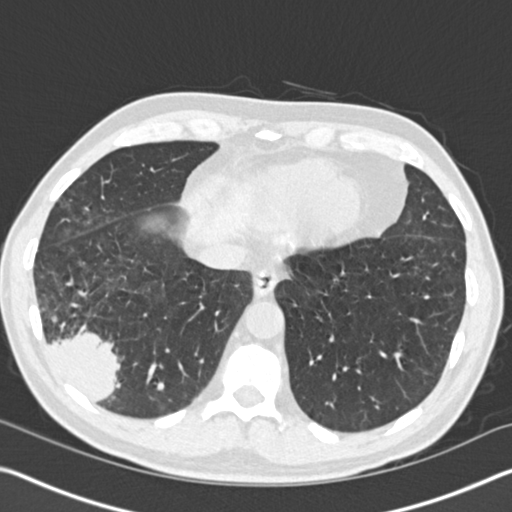
Axial slice from a low-dose chest CT screening exam. Baseline screening round. Lung window (W 1500 / L -600 HU). 2 mm slice thickness. Slice 117 of 161 in the series. 512 × 512 image matrix. Male participant, aged 61 years at enrolment. Current smoker at enrolment.
• Lesion marked by an expert reader, bounding box [x1, y1, x2, y2] px = [20, 288, 143, 417].
• Reader record for this screening exam (exam-level; its link to the box is not recorded): non-calcified nodule or mass ≥4 mm, right lower lobe, 52 × 36 mm, spiculated (stellate) margins, soft tissue attenuation.